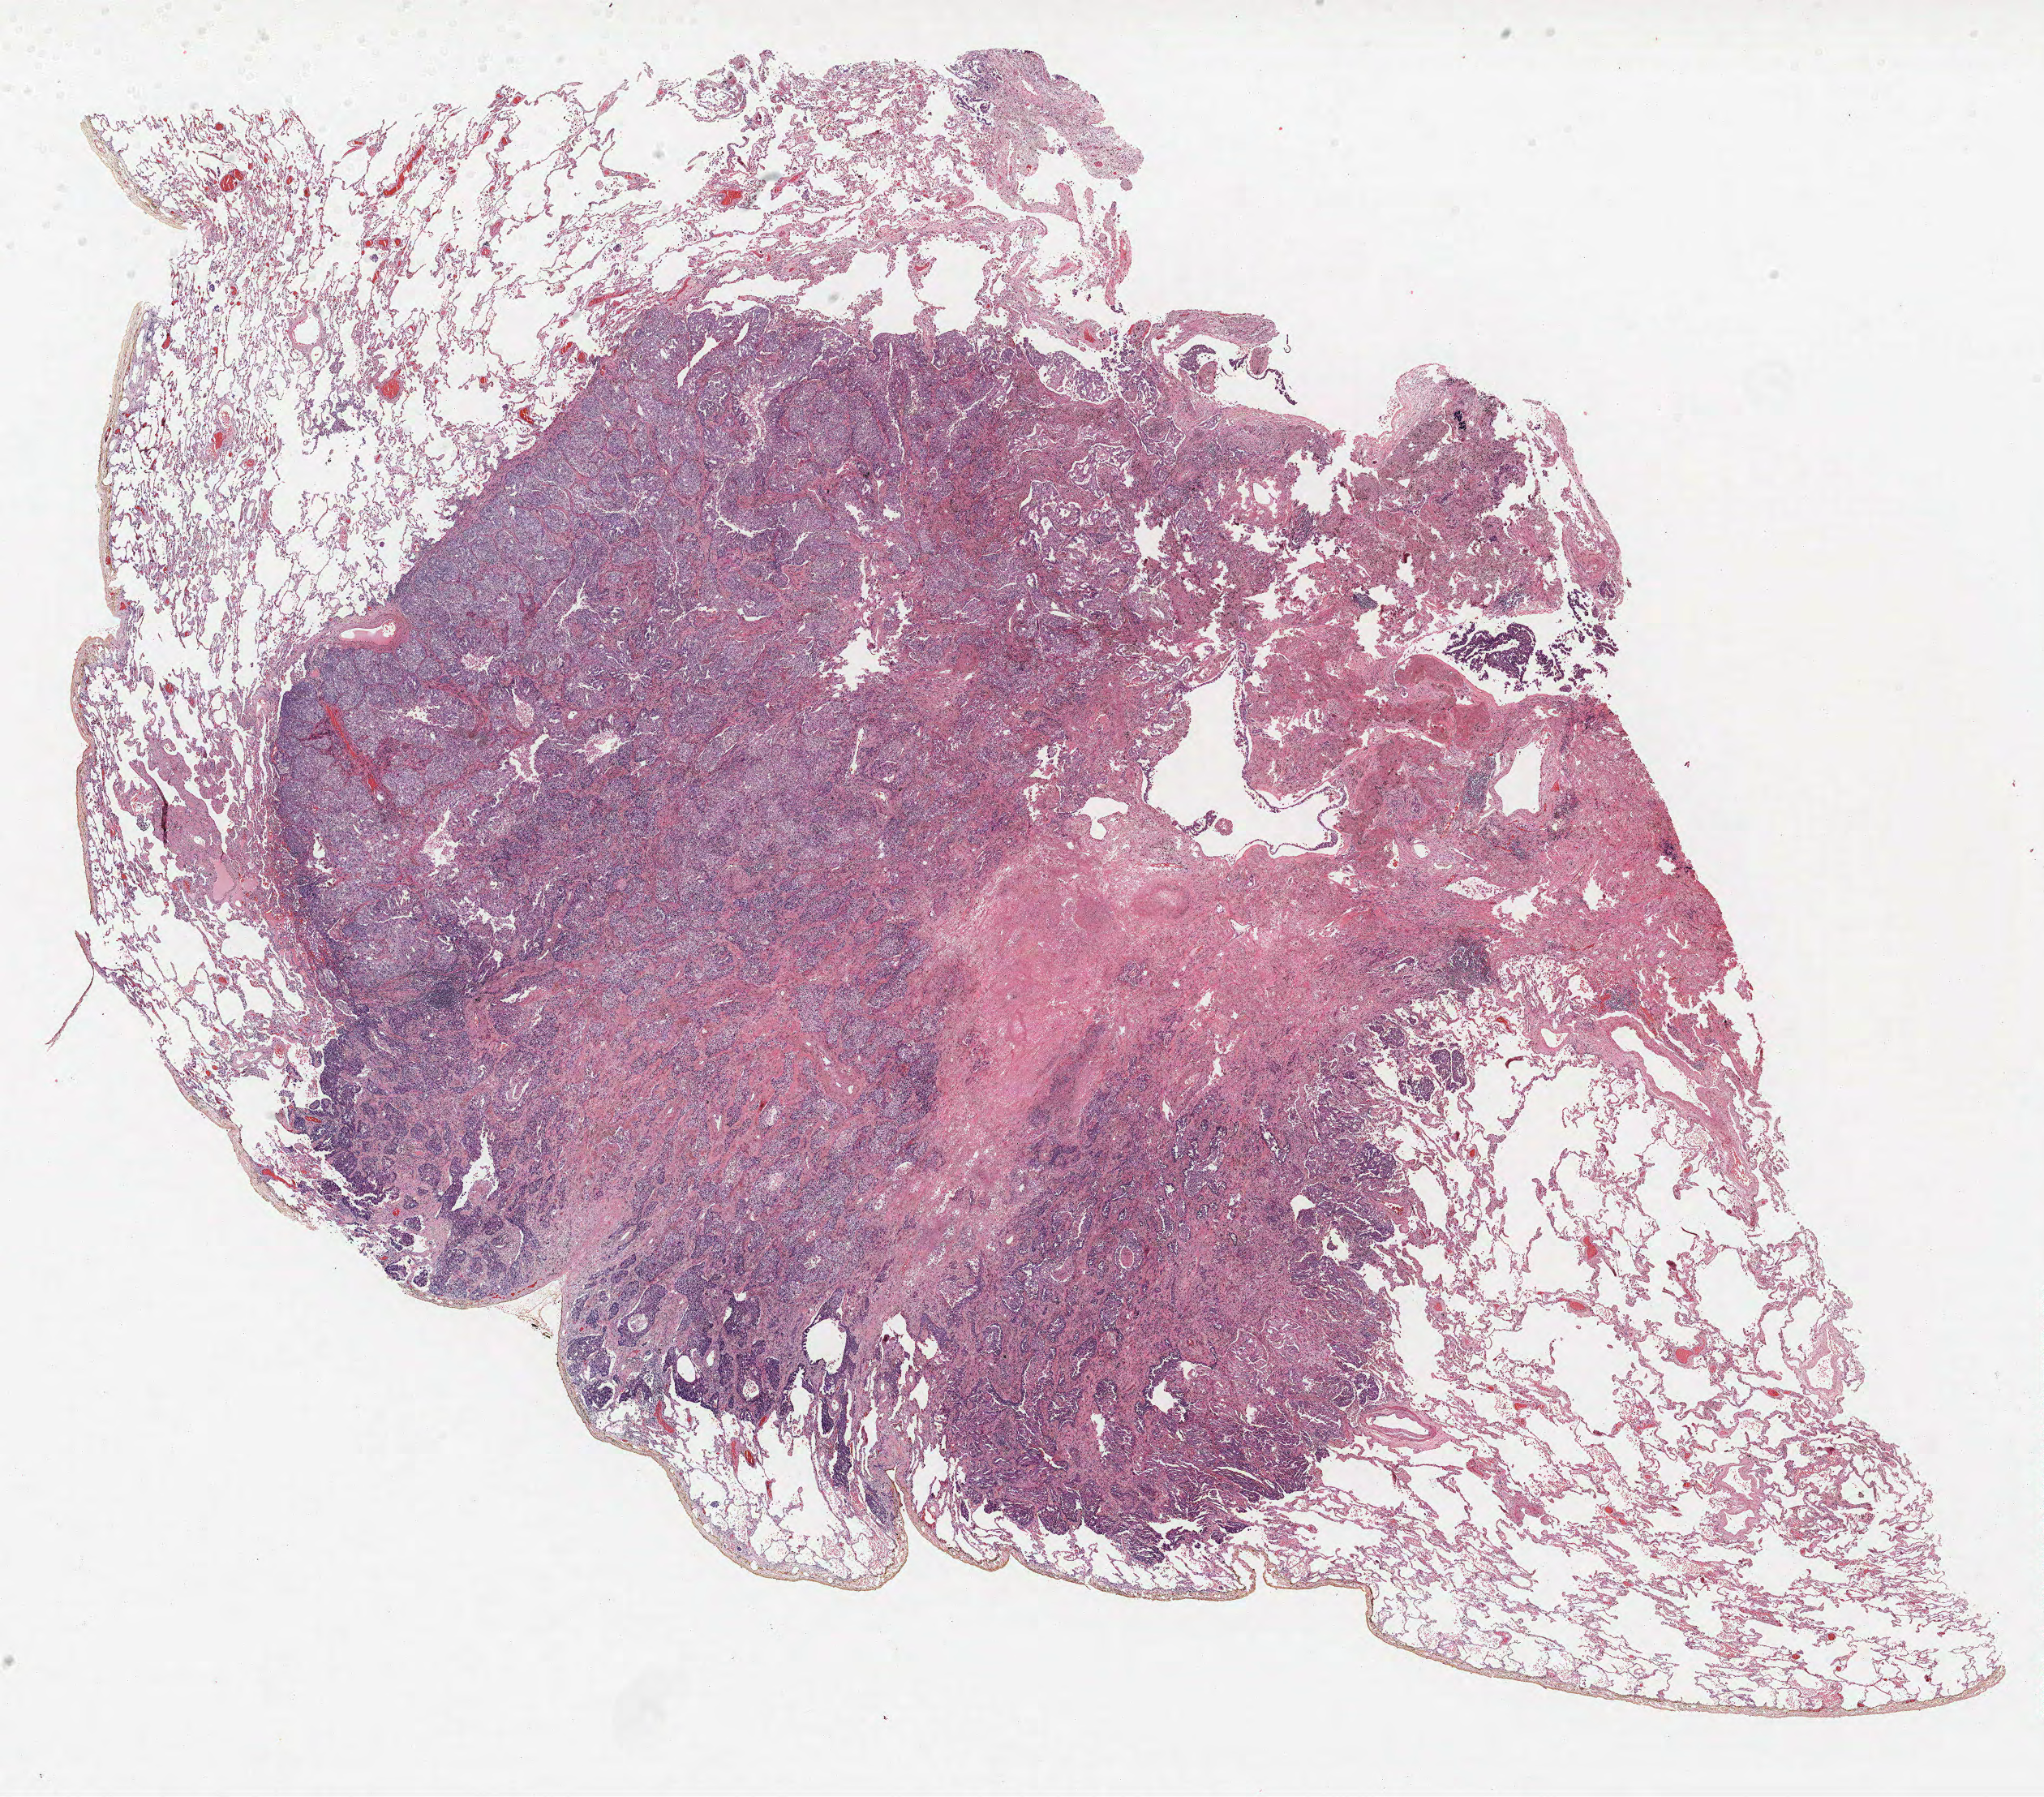
H&E-stained whole-slide image, low-resolution overview of the scanned area, about 20.2 x 17.7 mm; FFPE section; lung. Male patient, aged 63 at enrolment. Current smoker at enrolment. Grade: moderately differentiated (G2).
Participant's lung-cancer diagnosis: Adenocarcinoma, NOS (ICD-O-3 8140/3). Tumour size (pathology): 12 mm. Primary tumour location (clinical record): right lower lobe. Stage (AJCC 6th edition): IA. Note: participant had 3 primary lung cancers recorded; fields above describe the first.